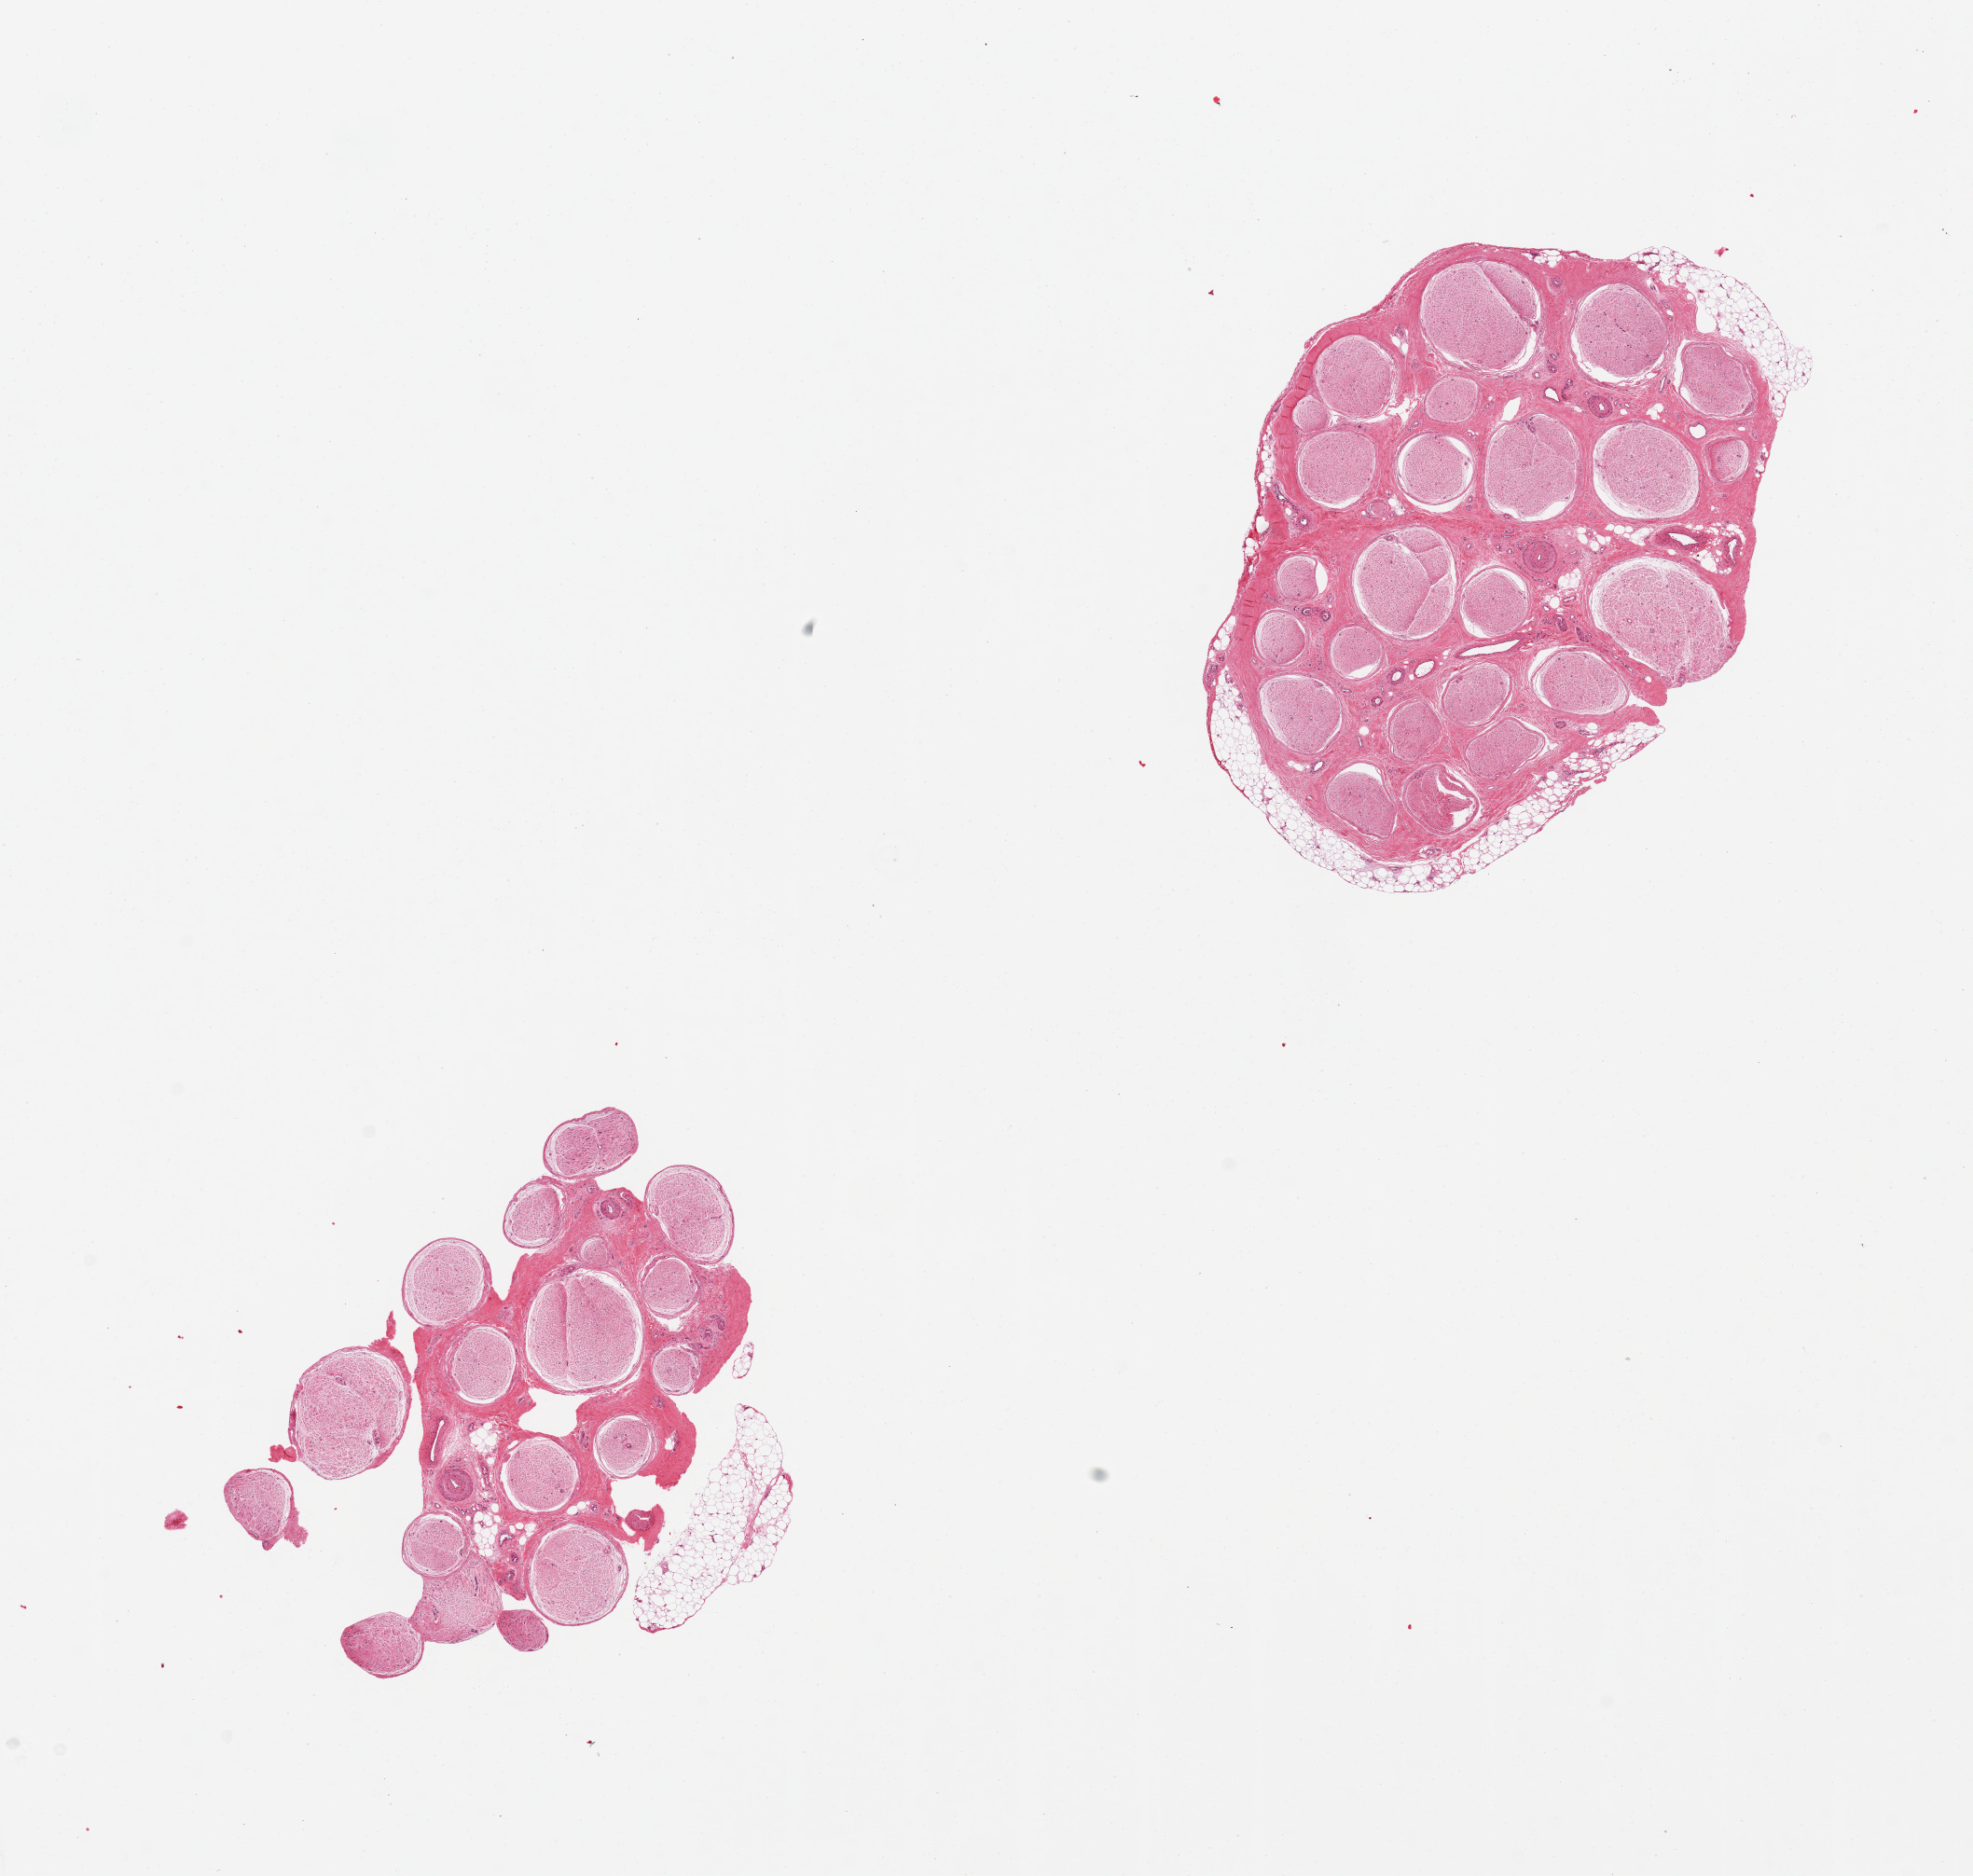
Digitized hematoxylin and eosin (H&E)-stained section — low-resolution overview of the scanned area, about 16.7 x 15.9 mm; PAXgene-fixed, paraffin-embedded tissue; sampled site (target tissue): tibial nerve; tissue donor sample. Male donor.
• review note (as recorded): 2 pieces, trace adherent nubbins of fat up to ~1mm; Good specimens